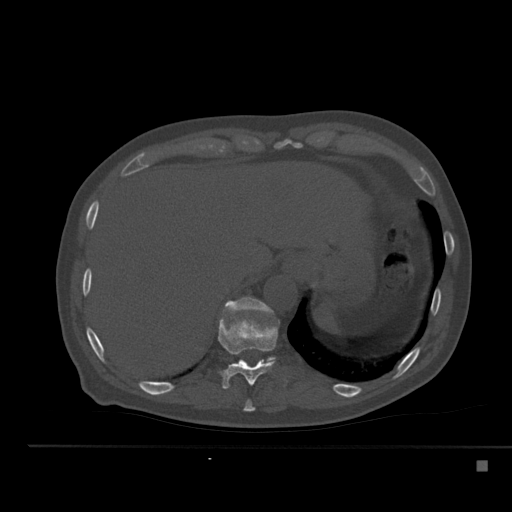
CT including the spine, one axial slice; slice 266 of 517 in the series (ordered by position); 120 kVp; bone window (W 1800 / L 400 HU); 1.5 mm slice thickness; 512 × 512 image matrix, field of view 408 × 408 mm. Male patient, age 70 years. From the clinical record (not read from this slice): primary cancer: renal; vertebrae with lytic lesions (as recorded): T4, T6, T10, T12, L3, L4, L5.
Annotated regions visible in this slice (semi-automatically segmented with operator editing):
- T10 vertebra: box from (x=218, y=319) to (x=278, y=389) px
- T11 vertebra: (x=222, y=297)–(x=275, y=361)
- T9 vertebra: (x=244, y=400)–(x=255, y=412)